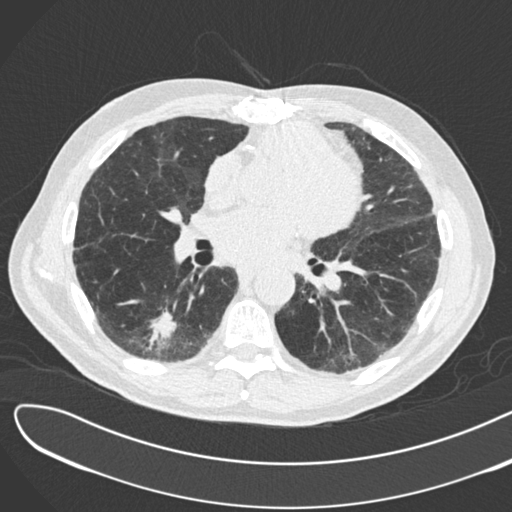
Axial slice from a low-dose chest CT screening exam; second annual screen; lung window (W 1500 / L -600 HU); 2 mm slice thickness; 120 kVp; slice 100 of 183 in the series. Male, age 72 years at enrolment.
Expert-annotated lung lesion, box from (x=127, y=289) to (x=196, y=354) px. The screening reader recorded 2 non-calcified nodules or masses ≥4 mm on this exam; which of them this box marks is not recorded. Participant outcome: lung cancer diagnosed 46 days after this screen — squamous cell carcinoma, NOS, right lower lobe, poorly differentiated (G3), stage IB (AJCC 6th edition), 42 mm at pathology.